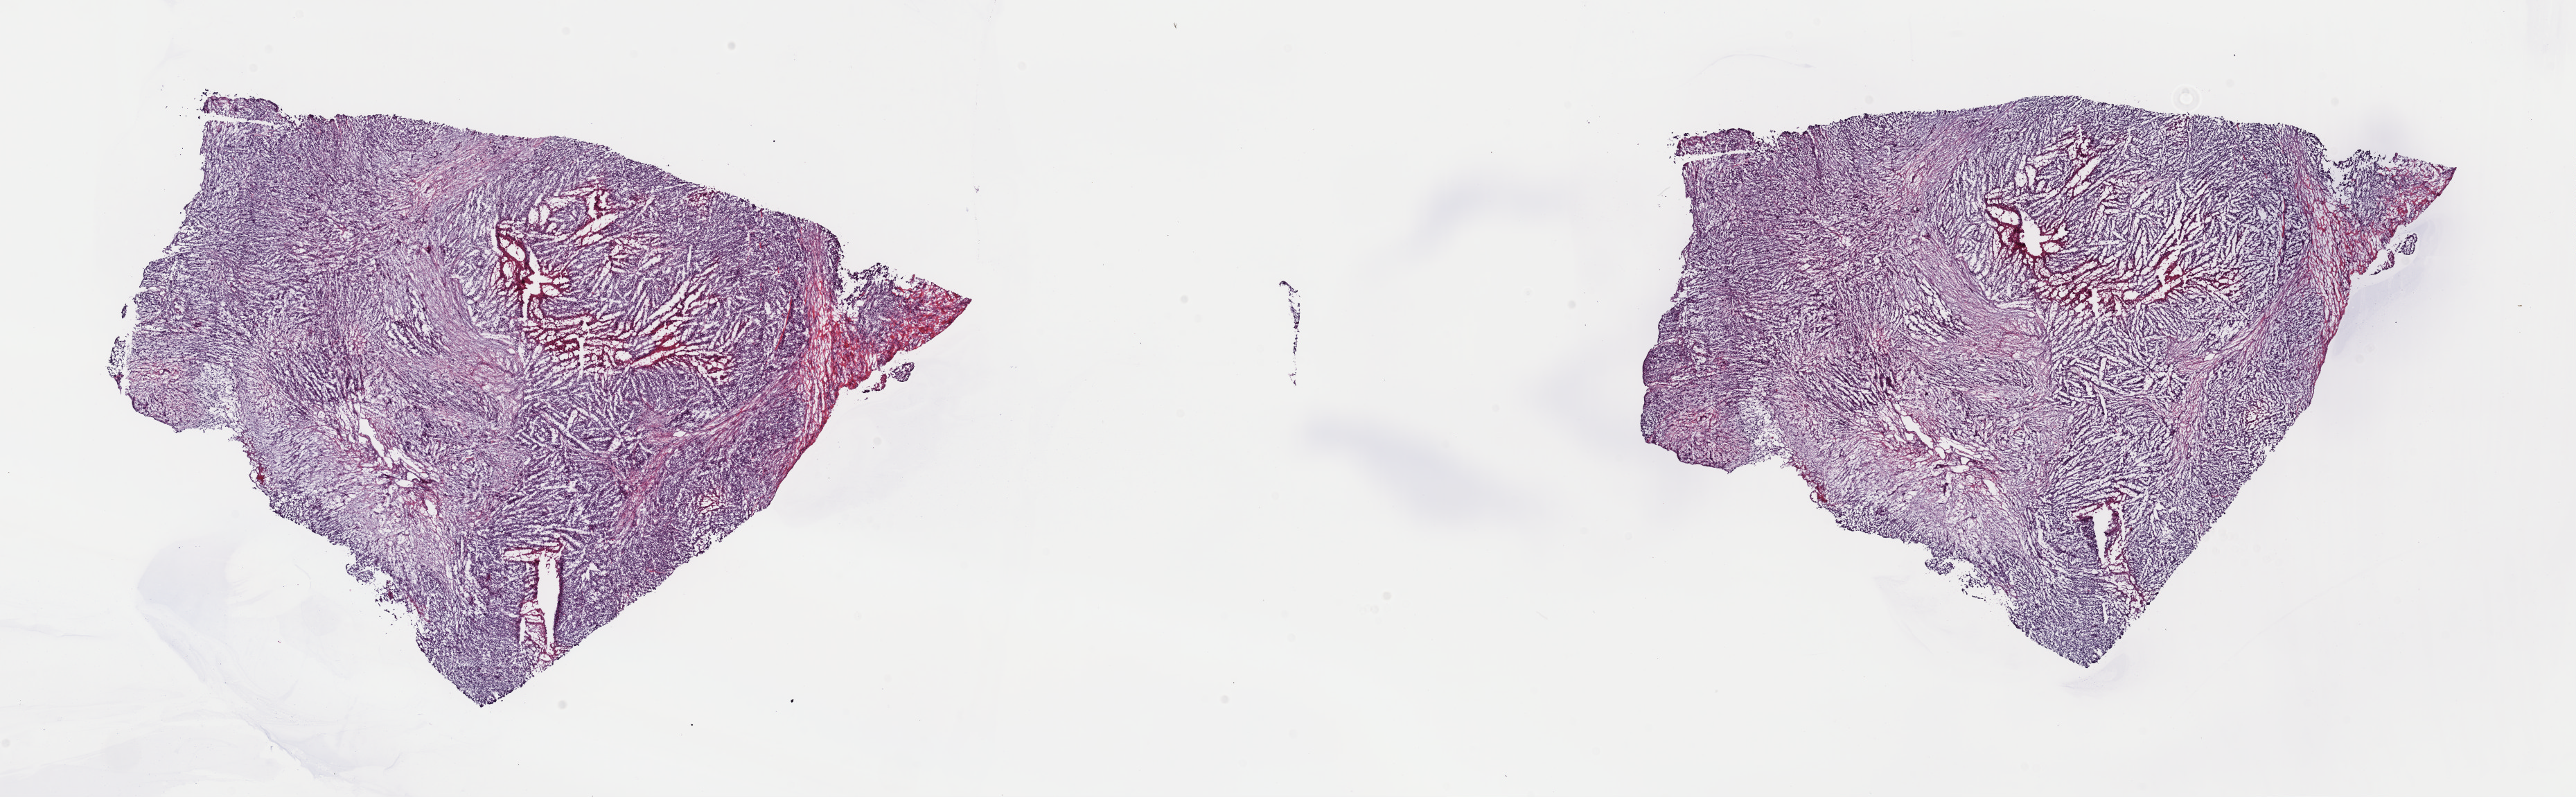
Whole-slide histology image, H&E-stained — a low-resolution overview of the entire scanned area, about 29.4 x 9.1 mm (slide scanned at 40x); frozen section from the top of the tissue portion; metastatic tumour sample, sampled site: connective, subcutaneous and other soft tissues of lower limb and hip. Male patient. Pathologist review of this section (percent, as recorded): tumour cells 90%, tumour nuclei 80%, normal cells 0%, stromal cells 0%, necrosis 10%. Infiltration values recorded for this section: lymphocyte infiltration 3%, monocyte infiltration 0%, neutrophil infiltration 0%.
- this section: metastatic tumour tissue
- patient diagnosis: Malignant melanoma, NOS